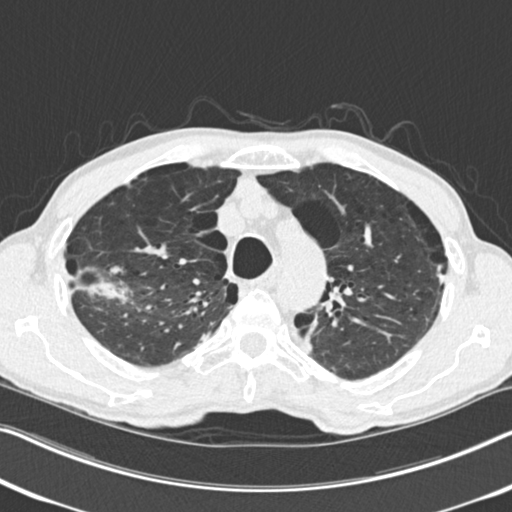
Axial slice from a low-dose chest CT screening exam, second annual screen, lung window (W 1500 / L -600 HU), 2 mm slice thickness, 512 × 512 image matrix, field of view 334 × 334 mm. Male, age 71 years at enrolment. Current smoker at enrolment.
Expert reader's lesion annotation, bounding box [x1, y1, x2, y2] px = [68, 248, 141, 319]. The screening reader recorded 4 non-calcified nodules or masses ≥4 mm on this exam (right upper lobe, right upper lobe, right upper lobe, left upper lobe); which of them this box marks is not recorded. Later outcome: lung cancer diagnosed 83 days after this screen — adenocarcinoma, NOS, right upper lobe, well differentiated (G1), stage IA (AJCC 6th edition), 30 mm at pathology.